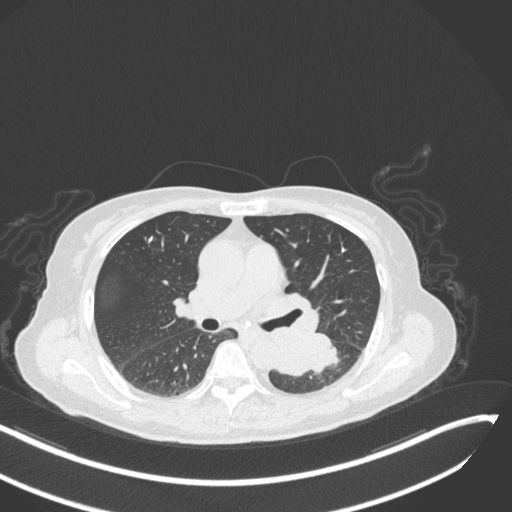
Chest CT, one axial slice. Slice 161 of 342 in the series (ordered by position). Reconstruction kernel B31f. Lung window (W 1500 / L -600 HU). 512 × 512 image matrix, field of view 400 × 400 mm. Female patient, age 64 years. From the clinical record (not read from this slice): clinical TNM (as recorded): T3 N1 M1; histopathological grade: G3.
Annotated regions visible in this slice (bounding box drawn by a radiologist):
- lung tumour (recorded histology: small cell carcinoma): bounding box <275,332,340,377> (left, top, right, bottom; pixels)